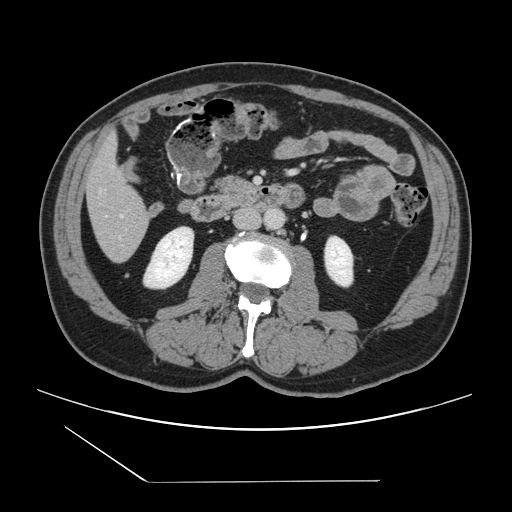
Contrast-enhanced abdominal CT, one axial slice. Position 35 of 157 along the scan axis. 120 kVp. Soft-tissue window (W 400 / L 40 HU). 512 × 512 image matrix. Male patient, age 61 years. Case-level facts recorded for this patient, not image findings: diagnosis: colorectal cancer liver metastases, imaged before liver resection; multiple liver metastases: yes; largest metastasis: 5.5 cm; chemotherapy before resection: no.
Outlined on this slice (expert manual segmentation):
- hepatic veins: box from (x=121, y=214) to (x=123, y=217) px
- liver: (x=85, y=139)–(x=150, y=262)
- planned liver remnant (the part of the liver to remain after resection): (x=85, y=138)–(x=146, y=219)